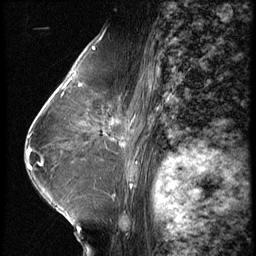
Breast MRI (dynamic contrast-enhanced), one sagittal slice. Slice 38 of 62 in the series (ordered by position). 3 images stored at this slice position (order not interpretable as contrast timing). 1.5 T. TE 4.2 ms, TR 9 ms. 256 × 256 image matrix. Patient: female, 65 years. From the clinical record (not read from this slice): setting: breast cancer imaged before/during neoadjuvant chemotherapy; receptor status: HR-positive, HER2-negative.
Outlined on this slice (semi-automatically segmented with operator editing):
- analysis volume of interest (the breast-tissue region the enhancement analysis was run in; not a lesion): box from (x=104, y=104) to (x=154, y=161) px
- tumour enhancement mask (voxels above the 140 % enhancement threshold inside the analysis volume of interest): (x=120, y=141)–(x=125, y=146)